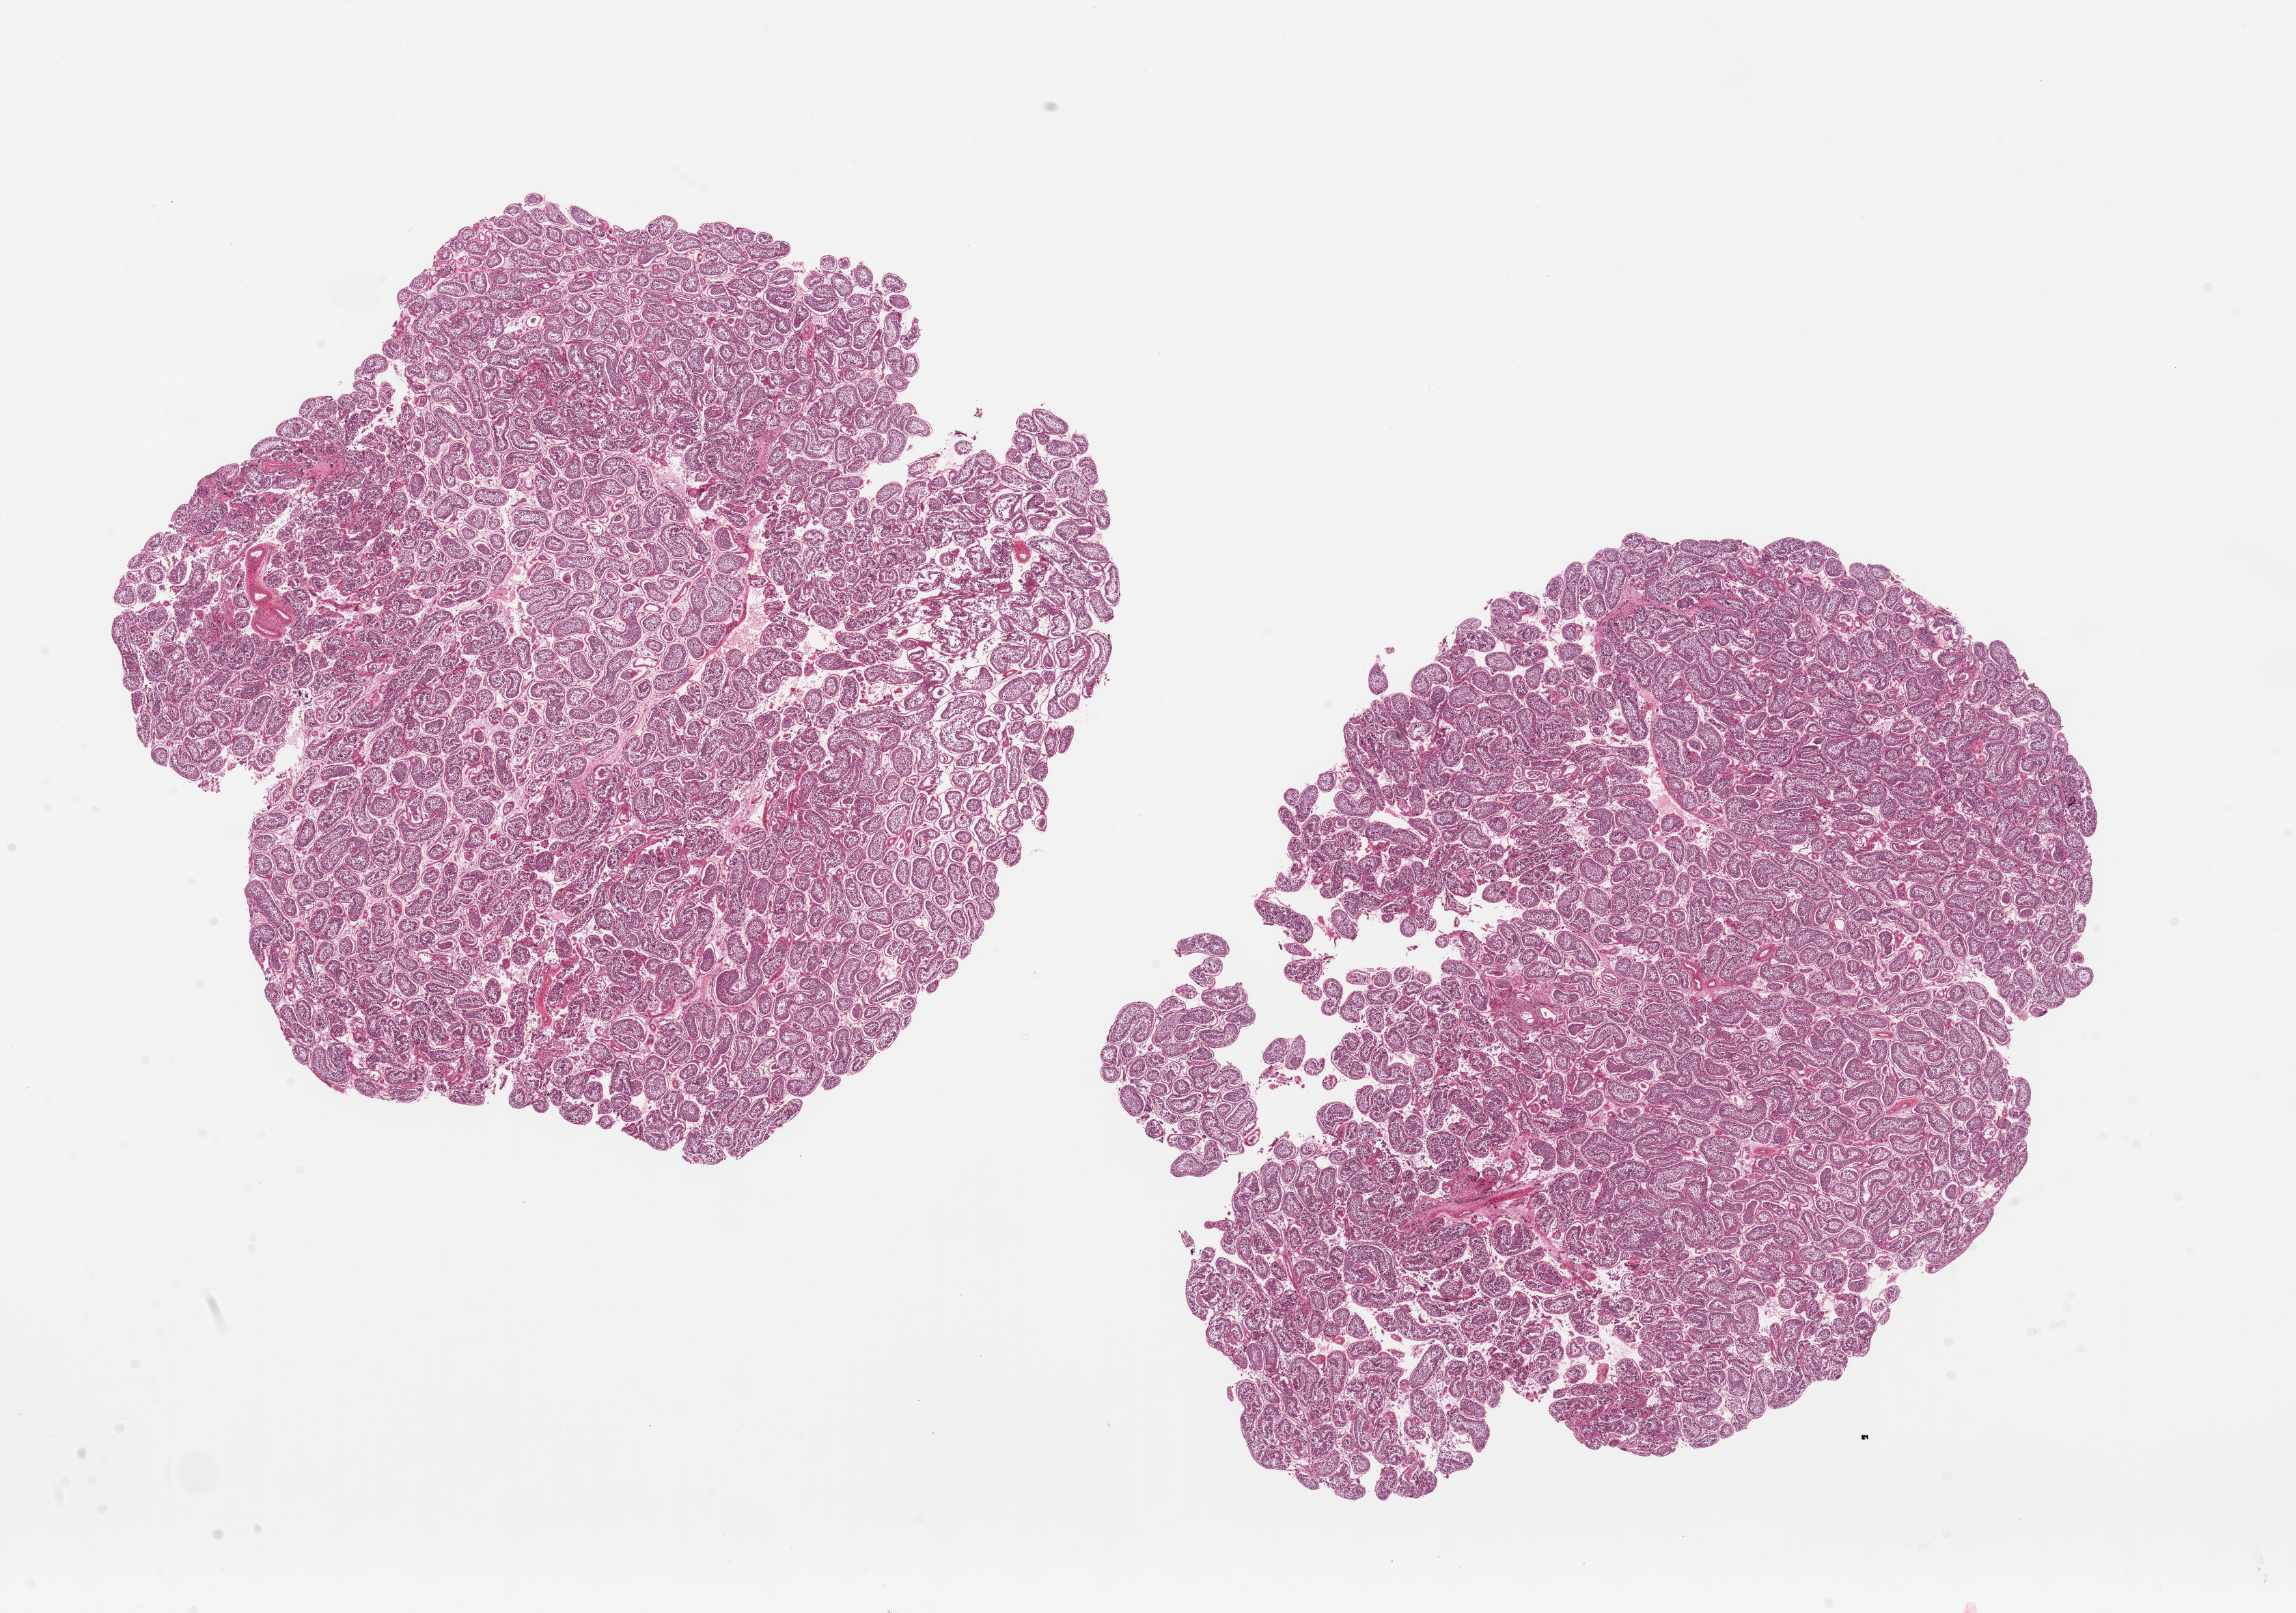
Whole-slide image, H&E stain — low-resolution overview of the scanned area, about 26.6 x 18.7 mm (acquisition: 20x scan). PAXgene-fixed, paraffin-embedded tissue. Section of testis (target tissue). Donor tissue sample.
Reviewer comment on this tissue sample: 2 pieces, spermatogenesis present.